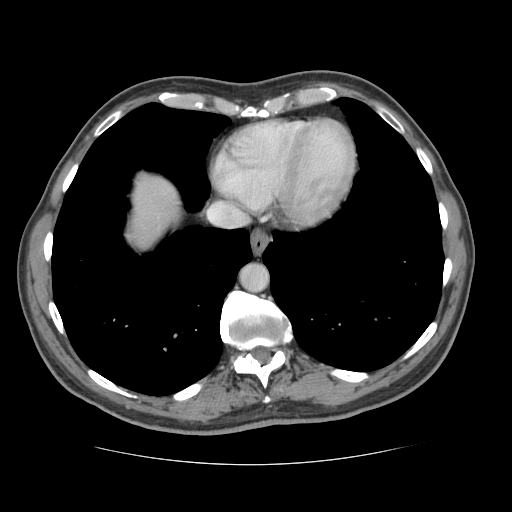
Contrast-enhanced abdominal CT, one axial slice. Position 122 of 134 along the scan axis. 120 kVp. Soft-tissue window (W 400 / L 40 HU). 2.5 mm slice thickness. 512 × 512 image matrix, field of view 377 × 377 mm. Male patient, age 68 years. From the clinical record (not read from this slice): diagnosis: colorectal cancer liver metastases, imaged before liver resection; multiple liver metastases: yes; largest metastasis: 2.2 cm.
Outlined on this slice (outlined manually by an expert reader):
- liver: box from (x=133, y=188) to (x=171, y=228) px
- planned liver remnant (the part of the liver to remain after resection): (x=133, y=189)–(x=170, y=228)